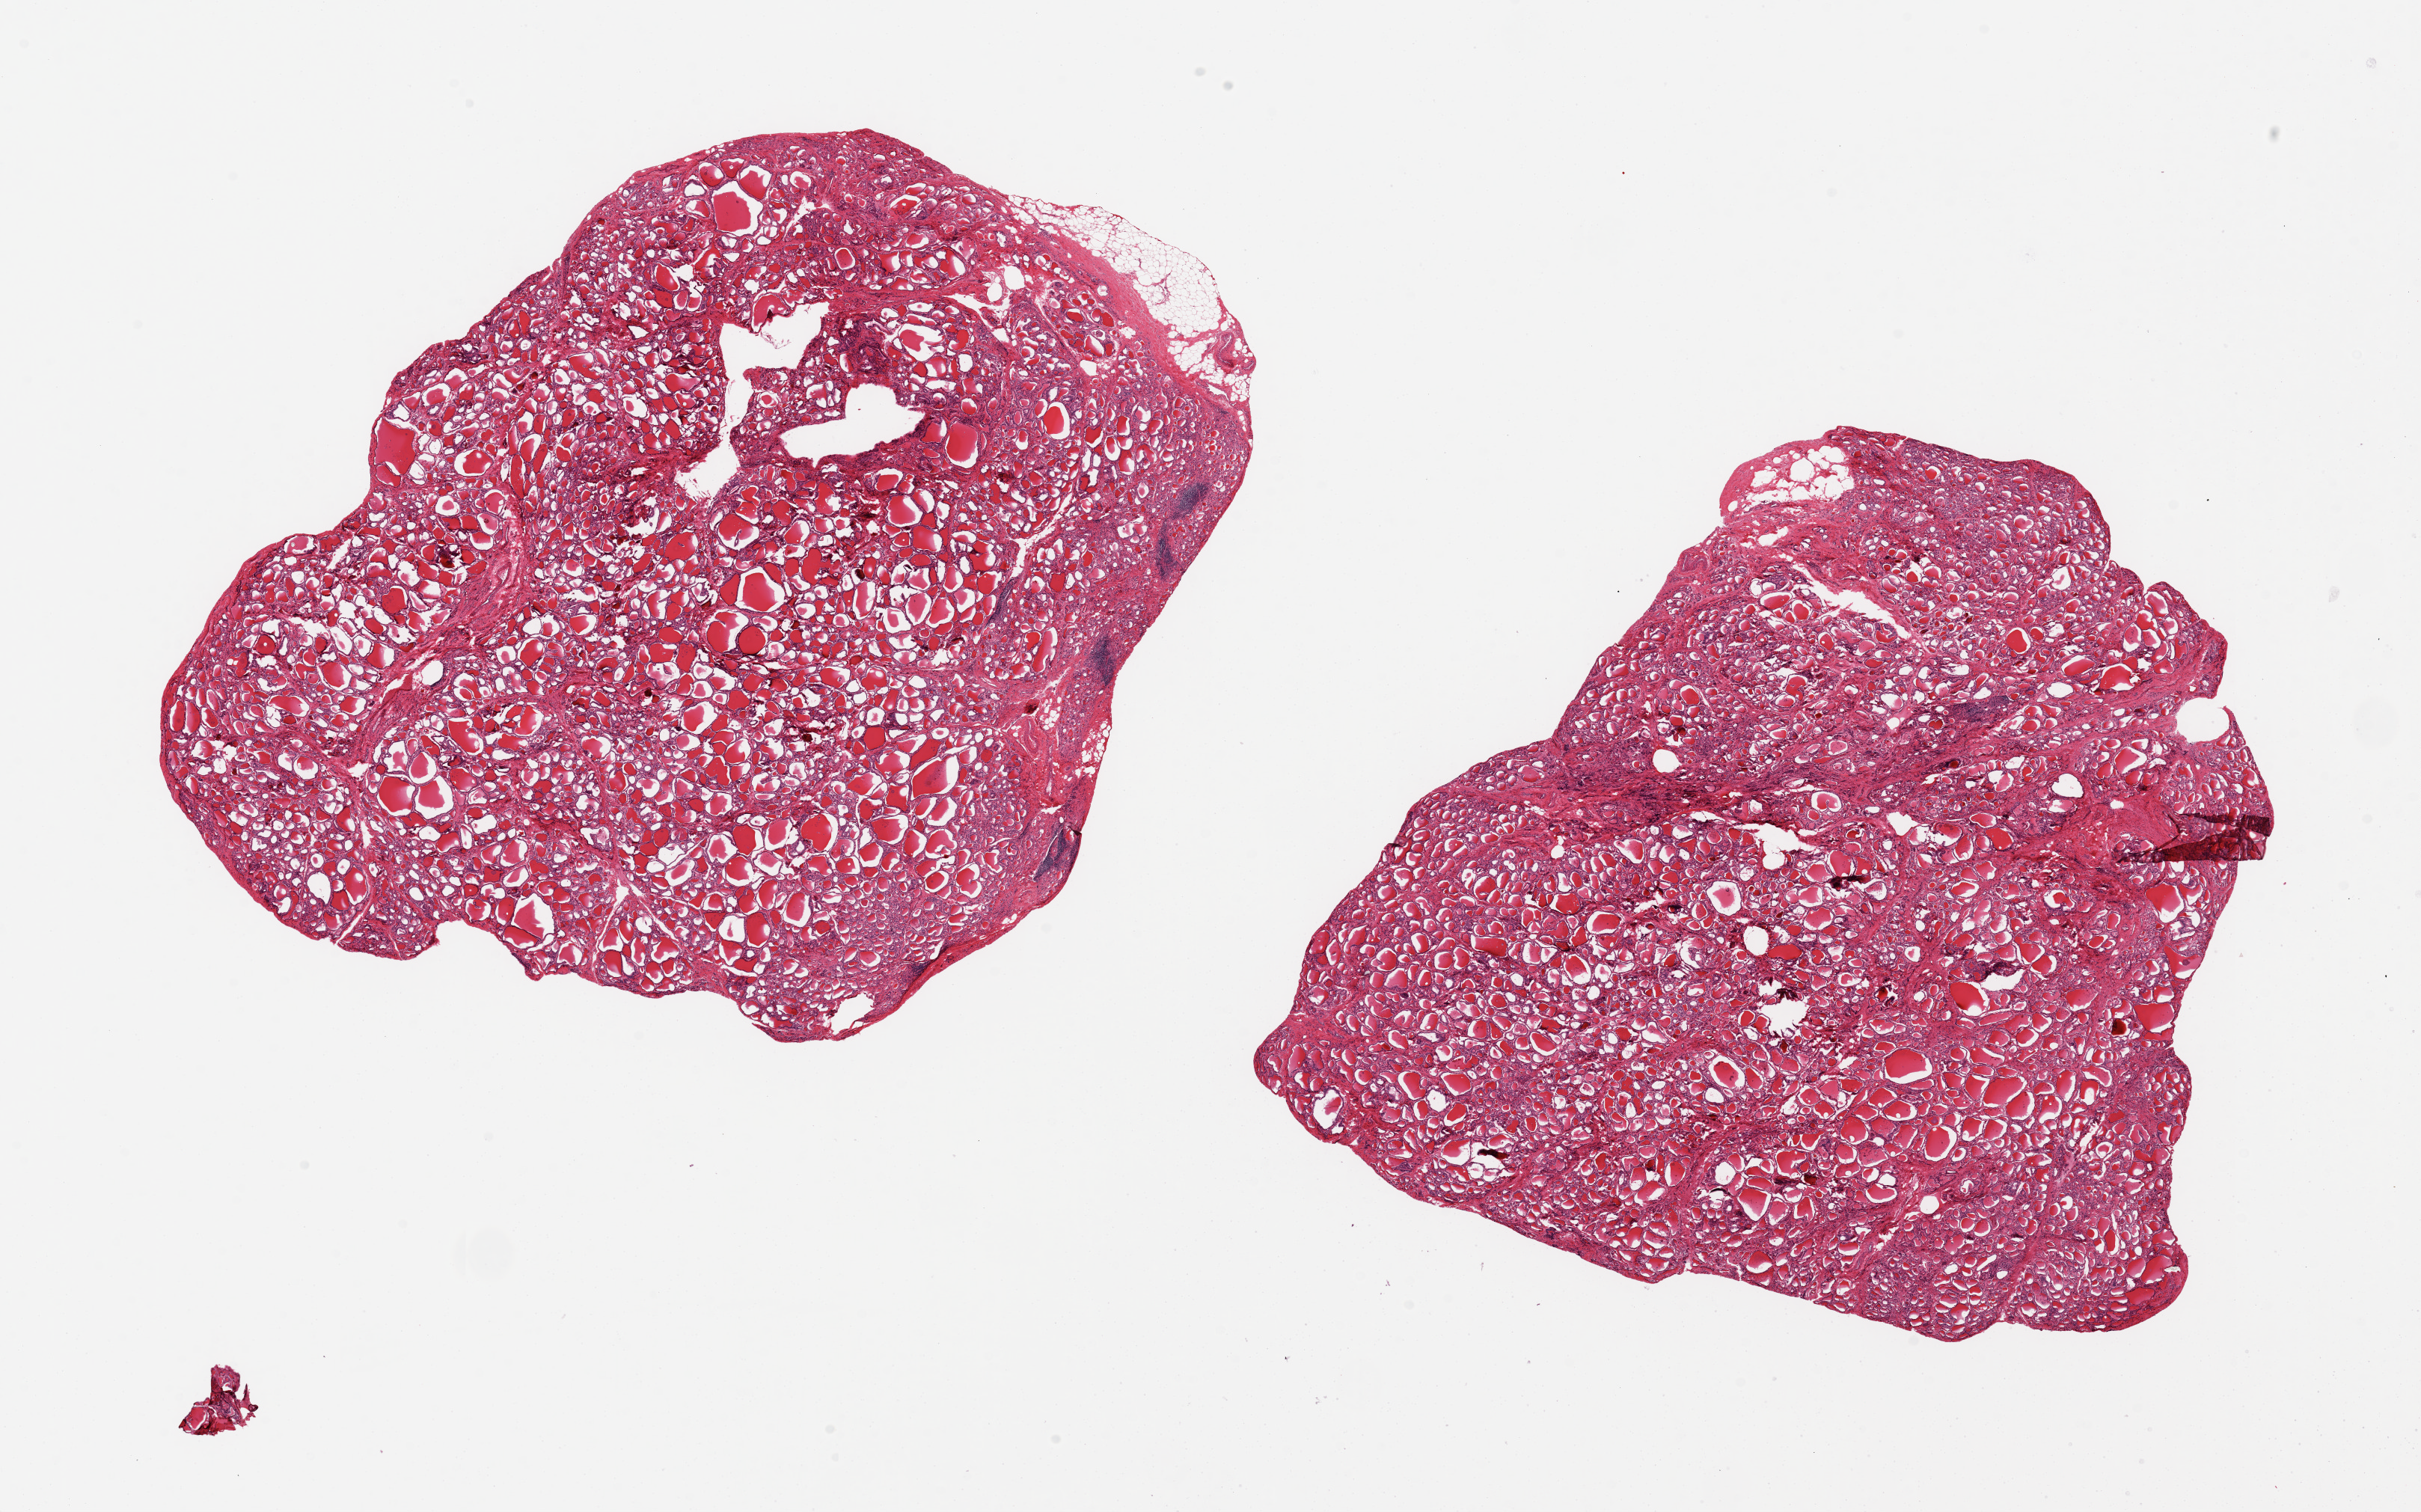
Digitized H&E-stained section, brightfield — low-resolution overview of the scanned area, about 25.6 x 16.0 mm (acquisition: 20x scan); PAXgene-fixed paraffin-embedded (PFPE) section; target tissue: thyroid; tissue donor sample. Donor: male.
* pathologist's review note for this sample: 2 pieces ~10x9mm. Patch Hashimoto's thyroiditis, regressive areas noted